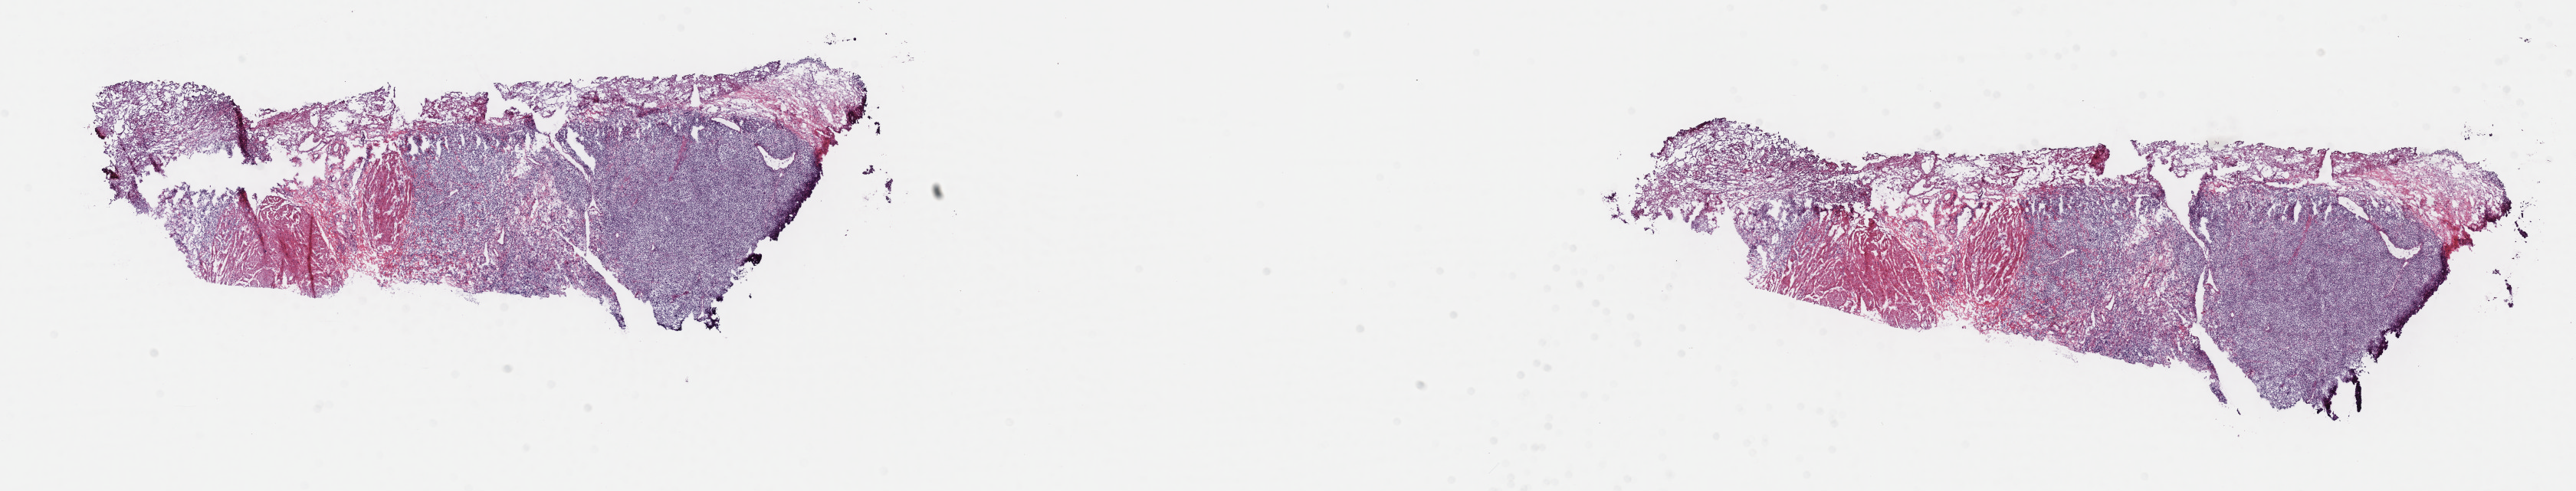
Hematoxylin and eosin (H&E) stained whole-slide image, whole scanned area (about 27.2 x 5.2 mm) shown as a low-resolution overview; frozen section from the top of the tissue portion; bladder, primary tumour sample. Patient: male, age at initial diagnosis 63 years. Histologic grade: high grade. Composition of this section per pathologist review: tumour cells 75%, tumour nuclei 65%, normal cells 25%, stromal cells 0%, necrosis 0%. Inflammatory infiltration, as recorded: lymphocyte infiltration 2%, monocyte infiltration 0%, neutrophil infiltration 0%.
AJCC pathologic stage: II (7th edition). Pathologic diagnosis: Transitional cell carcinoma.